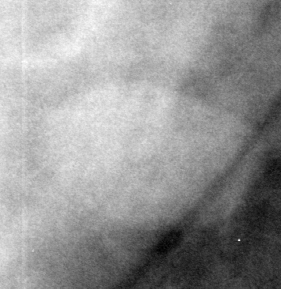
Cropped region of a digitized screen-film mammogram centred on a radiologist-marked abnormality, left breast, MLO view, BI-RADS breast density category 3 (scale 1–4).
Marked abnormality: mass, shape oval, margins circumscribed; BI-RADS assessment category 3; pathology (as recorded): benign.